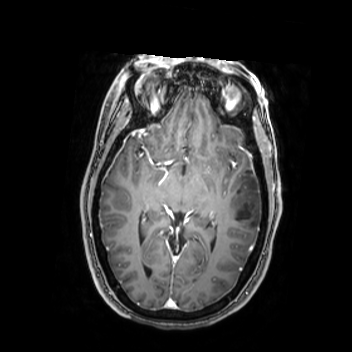
Brain MRI from a brain-tumour surgery series, one axial slice. Slice 150 of 350 in the series (ordered by position). T1-weighted post-contrast. 352 × 352 image matrix, field of view 280 × 280 mm. From the clinical record (not read from this slice): histopathology: Oligodendroglioma; WHO grade: 2; IDH mutation: yes.
Structures marked on this image (manually delineated by an expert):
- tumour: bounding box [x1, y1, x2, y2] px = [224, 174, 262, 232]